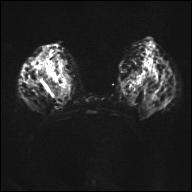
Breast MRI, one axial slice; slice 20 of 32 in the series (ordered by position); diffusion-weighted series; image 2 of 4 stored at this slice position (different b-values; order by instance number); 1.5 T; 4 mm slice thickness; 192 × 192 image matrix, field of view 360 × 360 mm. Female patient.
Structures marked on this image (manually delineated by an expert):
- tumour on diffusion-weighted imaging: box from (x=36, y=46) to (x=64, y=100) px